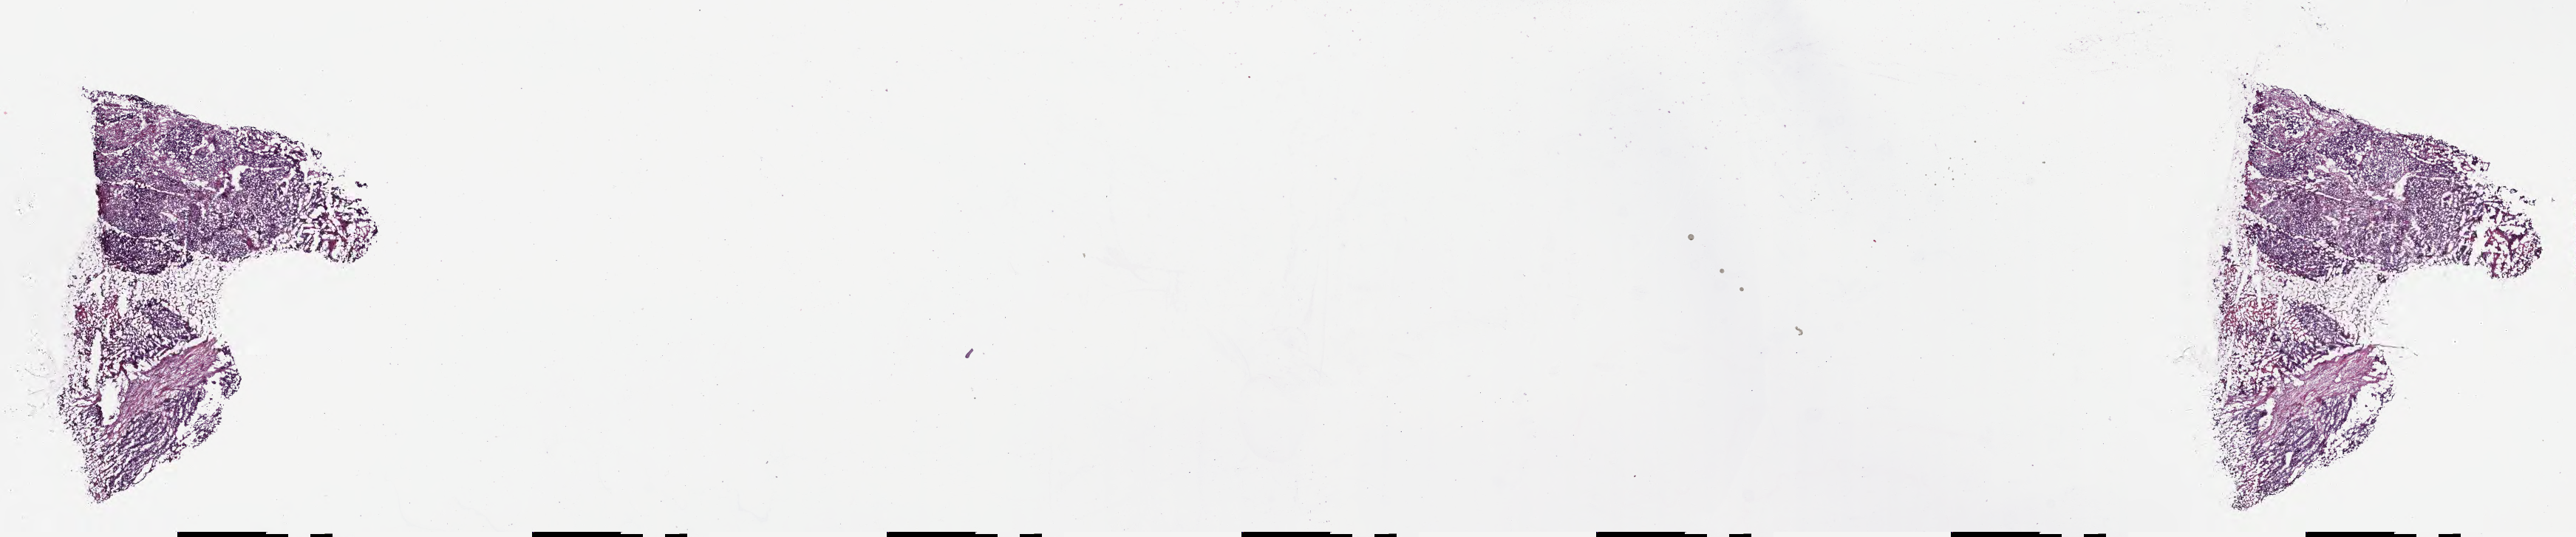
Whole-slide image, H&E stain of tumor tissue from the prostate, a low-resolution overview of the entire scanned area, about 28.2 x 5.9 mm; cryosection (OCT / tissue freezing medium). Patient: male, age 195 months (16 years 3 months).
Diagnosis (ICD-O-3 morphology term): Neoplasm, uncertain whether benign or malignant.